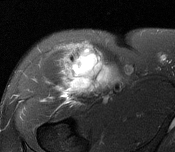
MRI of an extremity soft-tissue mass, one axial slice. Slice 108 of 116 in the series (ordered by position). T2-weighted fat-saturated. MR volume resampled by the dataset authors to the PET/CT grid (not the native acquisition matrix). 3.27 mm slice thickness. 175 × 152 image matrix, field of view 171 × 148 mm. Male patient. Case-level facts recorded for this patient, not image findings: histological type: pleiomorphic leiomyosarcoma; grade: intermediate; site of the primary tumour: right thigh.
Outlined on this slice (expert contour drawn on MRI and transferred to this co-registered scan by the dataset authors):
- gross tumour volume including surrounding oedema: bounding box (x1, y1, x2, y2) in pixels: (58, 45, 112, 96)
- gross tumour volume (mass): (65, 54, 109, 94)